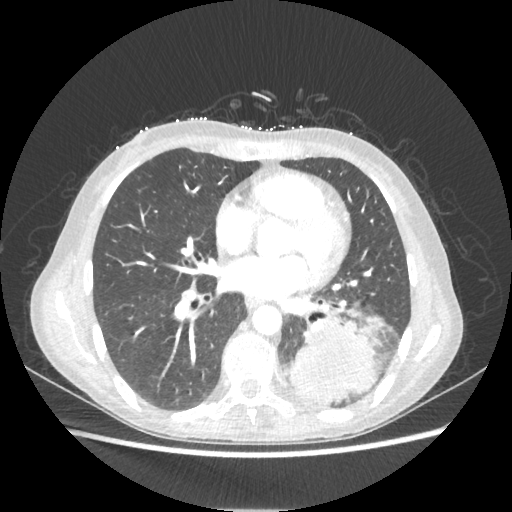
Chest CT, one axial slice; position 100 of 221 along the scan axis; 80 kVp; lung window (W 1500 / L -600 HU); 512 × 512 image matrix, field of view 360 × 360 mm. Patient: female, 53 years. Case-level facts recorded for this patient, not image findings: clinical TNM (as recorded): T3 N0 M0.
Annotated regions visible in this slice (rectangle marked by the reading radiologist):
- lung tumour (recorded histology: adenocarcinoma): box from (x=287, y=316) to (x=377, y=404) px